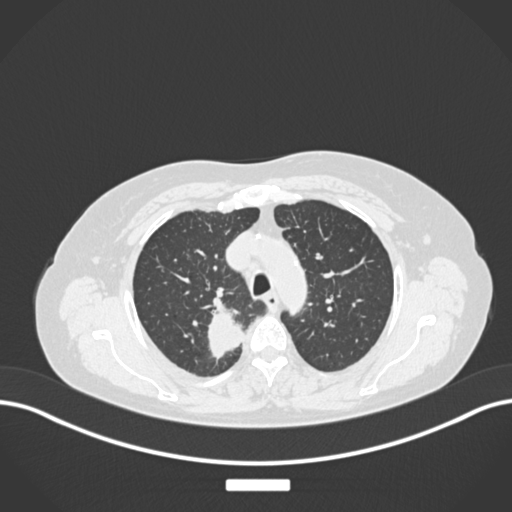
Chest CT, one axial slice. Position 194 of 237 along the scan axis. Lung window (W 1500 / L -600 HU). 1 mm slice thickness. 512 × 512 image matrix, field of view 400 × 400 mm. Patient: female, 62 years. From the clinical record (not read from this slice): clinical TNM (as recorded): T1c N1 M0.
Annotated regions visible in this slice (rectangle marked by the reading radiologist):
- lung tumour (recorded histology: squamous cell carcinoma): box from (x=208, y=303) to (x=244, y=364) px